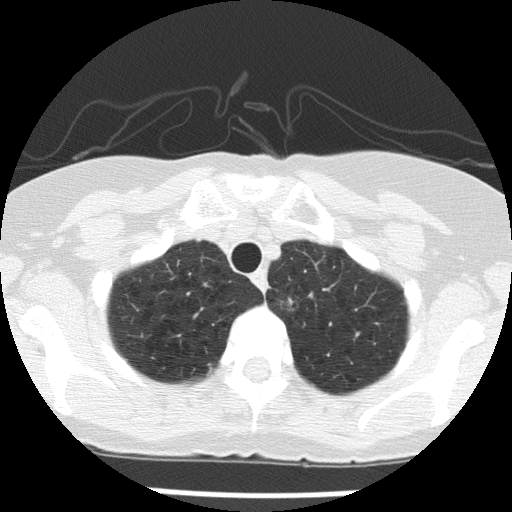
Low-dose screening chest CT, one axial slice; slice 123 of 143 in the series (ordered by position); reconstruction kernel FC51; lung window (W 1500 / L -600 HU); 512 × 512 image matrix, field of view 276 × 276 mm.
Outlined on this slice (manually delineated by an expert):
- lesion 1 (tumor, upper lobe of left lung): box from (x=289, y=299) to (x=292, y=304) px